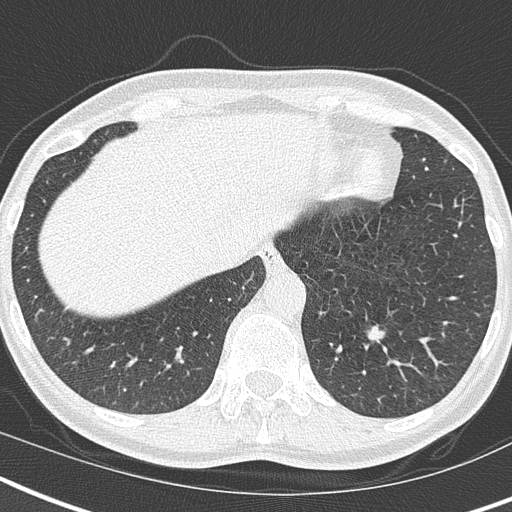
Low-dose screening chest CT, axial slice, third screening round (two years after baseline), lung window (W 1500 / L -600 HU), lung (sharp) reconstruction kernel (B50f), 120 kVp, slice 129 of 173 in the series, 512 × 512 image matrix, field of view 293 × 293 mm. Female, age 55 years at enrolment. Current smoker at enrolment.
Expert-annotated lung lesion, bounding box (x1, y1, x2, y2) in pixels: (349, 309, 403, 359). The screening reader recorded 2 non-calcified nodules or masses ≥4 mm on this exam; which of them this box marks is not recorded. Lung cancer was diagnosed 349 days after this screen: adenocarcinoma, NOS, left lower lobe, well differentiated (G1), stage IA (AJCC 6th edition), 11 mm at pathology.